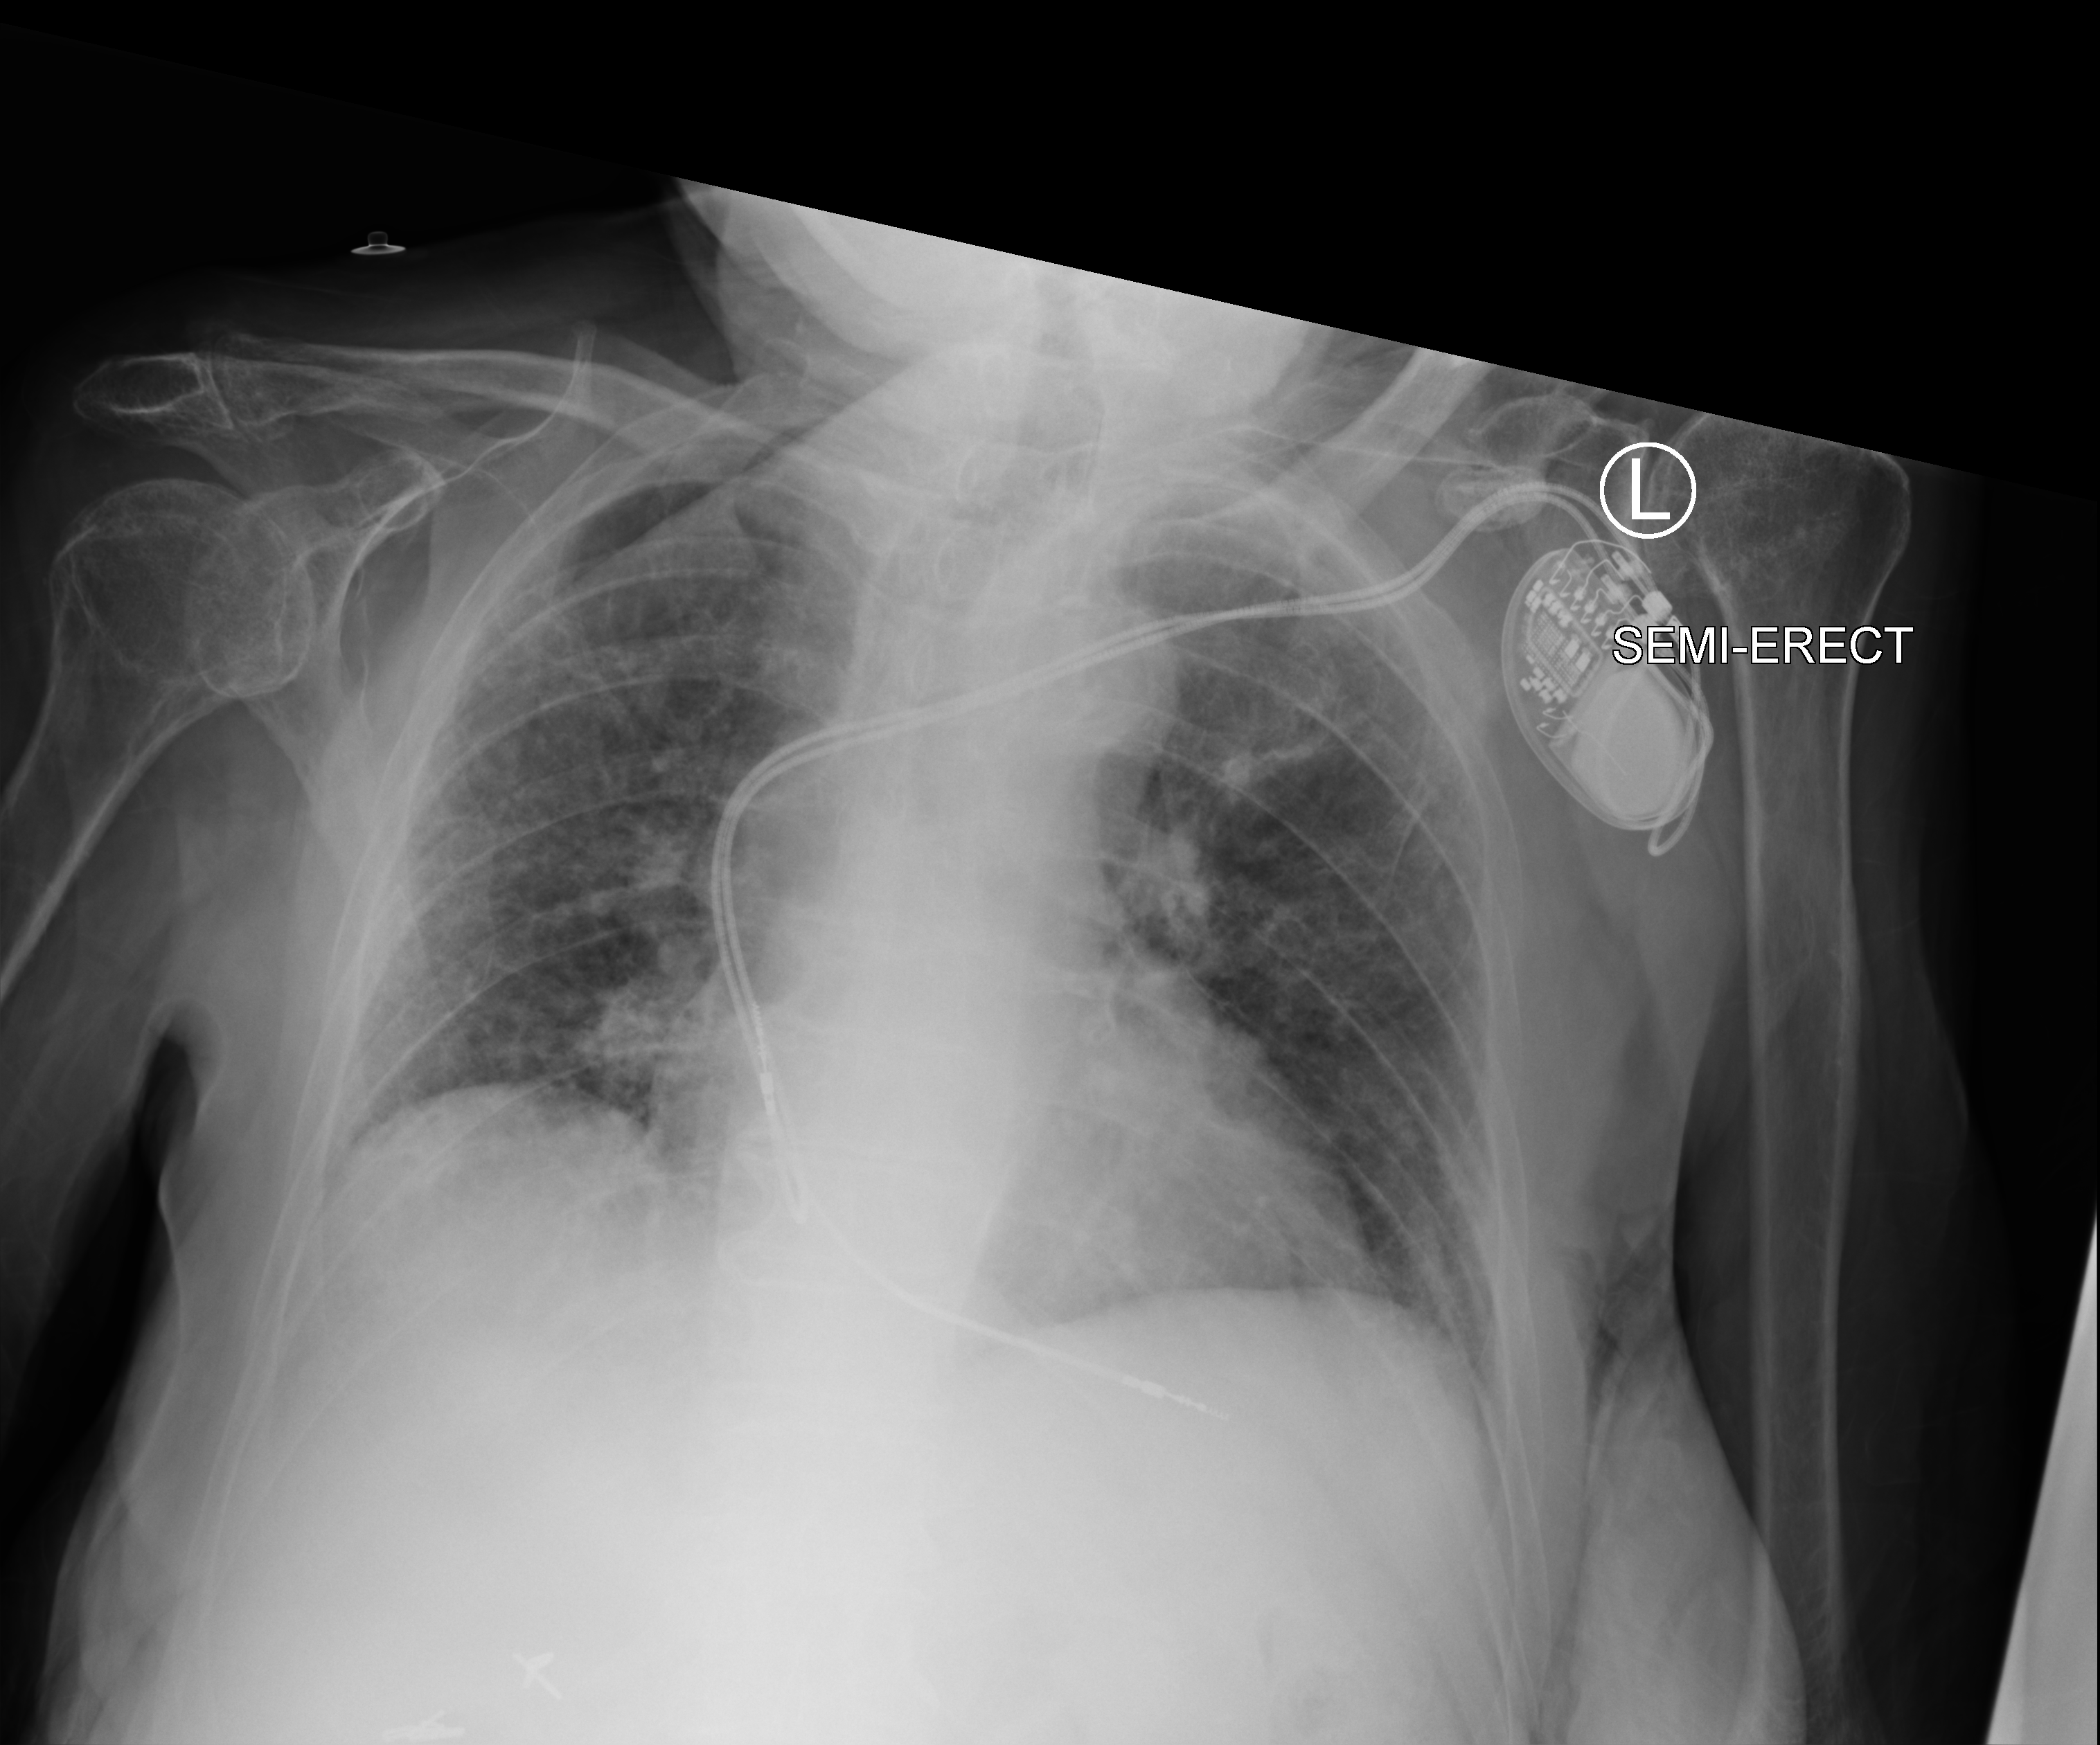
Portable chest radiograph, anteroposterior (AP) projection. Female patient hospitalised with COVID-19, age 75–90 years.
Hospital-stay facts (about this admission, not read from this image; timing relative to this image not recorded): mechanically ventilated during this hospital stay: no; admitted to intensive care during this hospital stay: no.